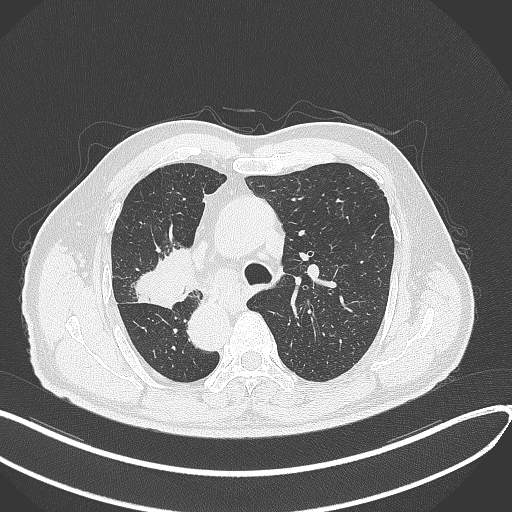
Chest CT, one axial slice. Slice 210 of 300 in the series (ordered by position). Reconstruction kernel B70f. Lung window (W 1500 / L -600 HU). 1 mm slice thickness. 512 × 512 image matrix, field of view 400 × 400 mm. Male patient, age 67 years. From the clinical record (not read from this slice): clinical TNM (as recorded): T2a N0 M0.
Outlined on this slice (rectangle marked by the reading radiologist):
- lung tumour (recorded histology: squamous cell carcinoma): box from (x=131, y=249) to (x=196, y=310) px